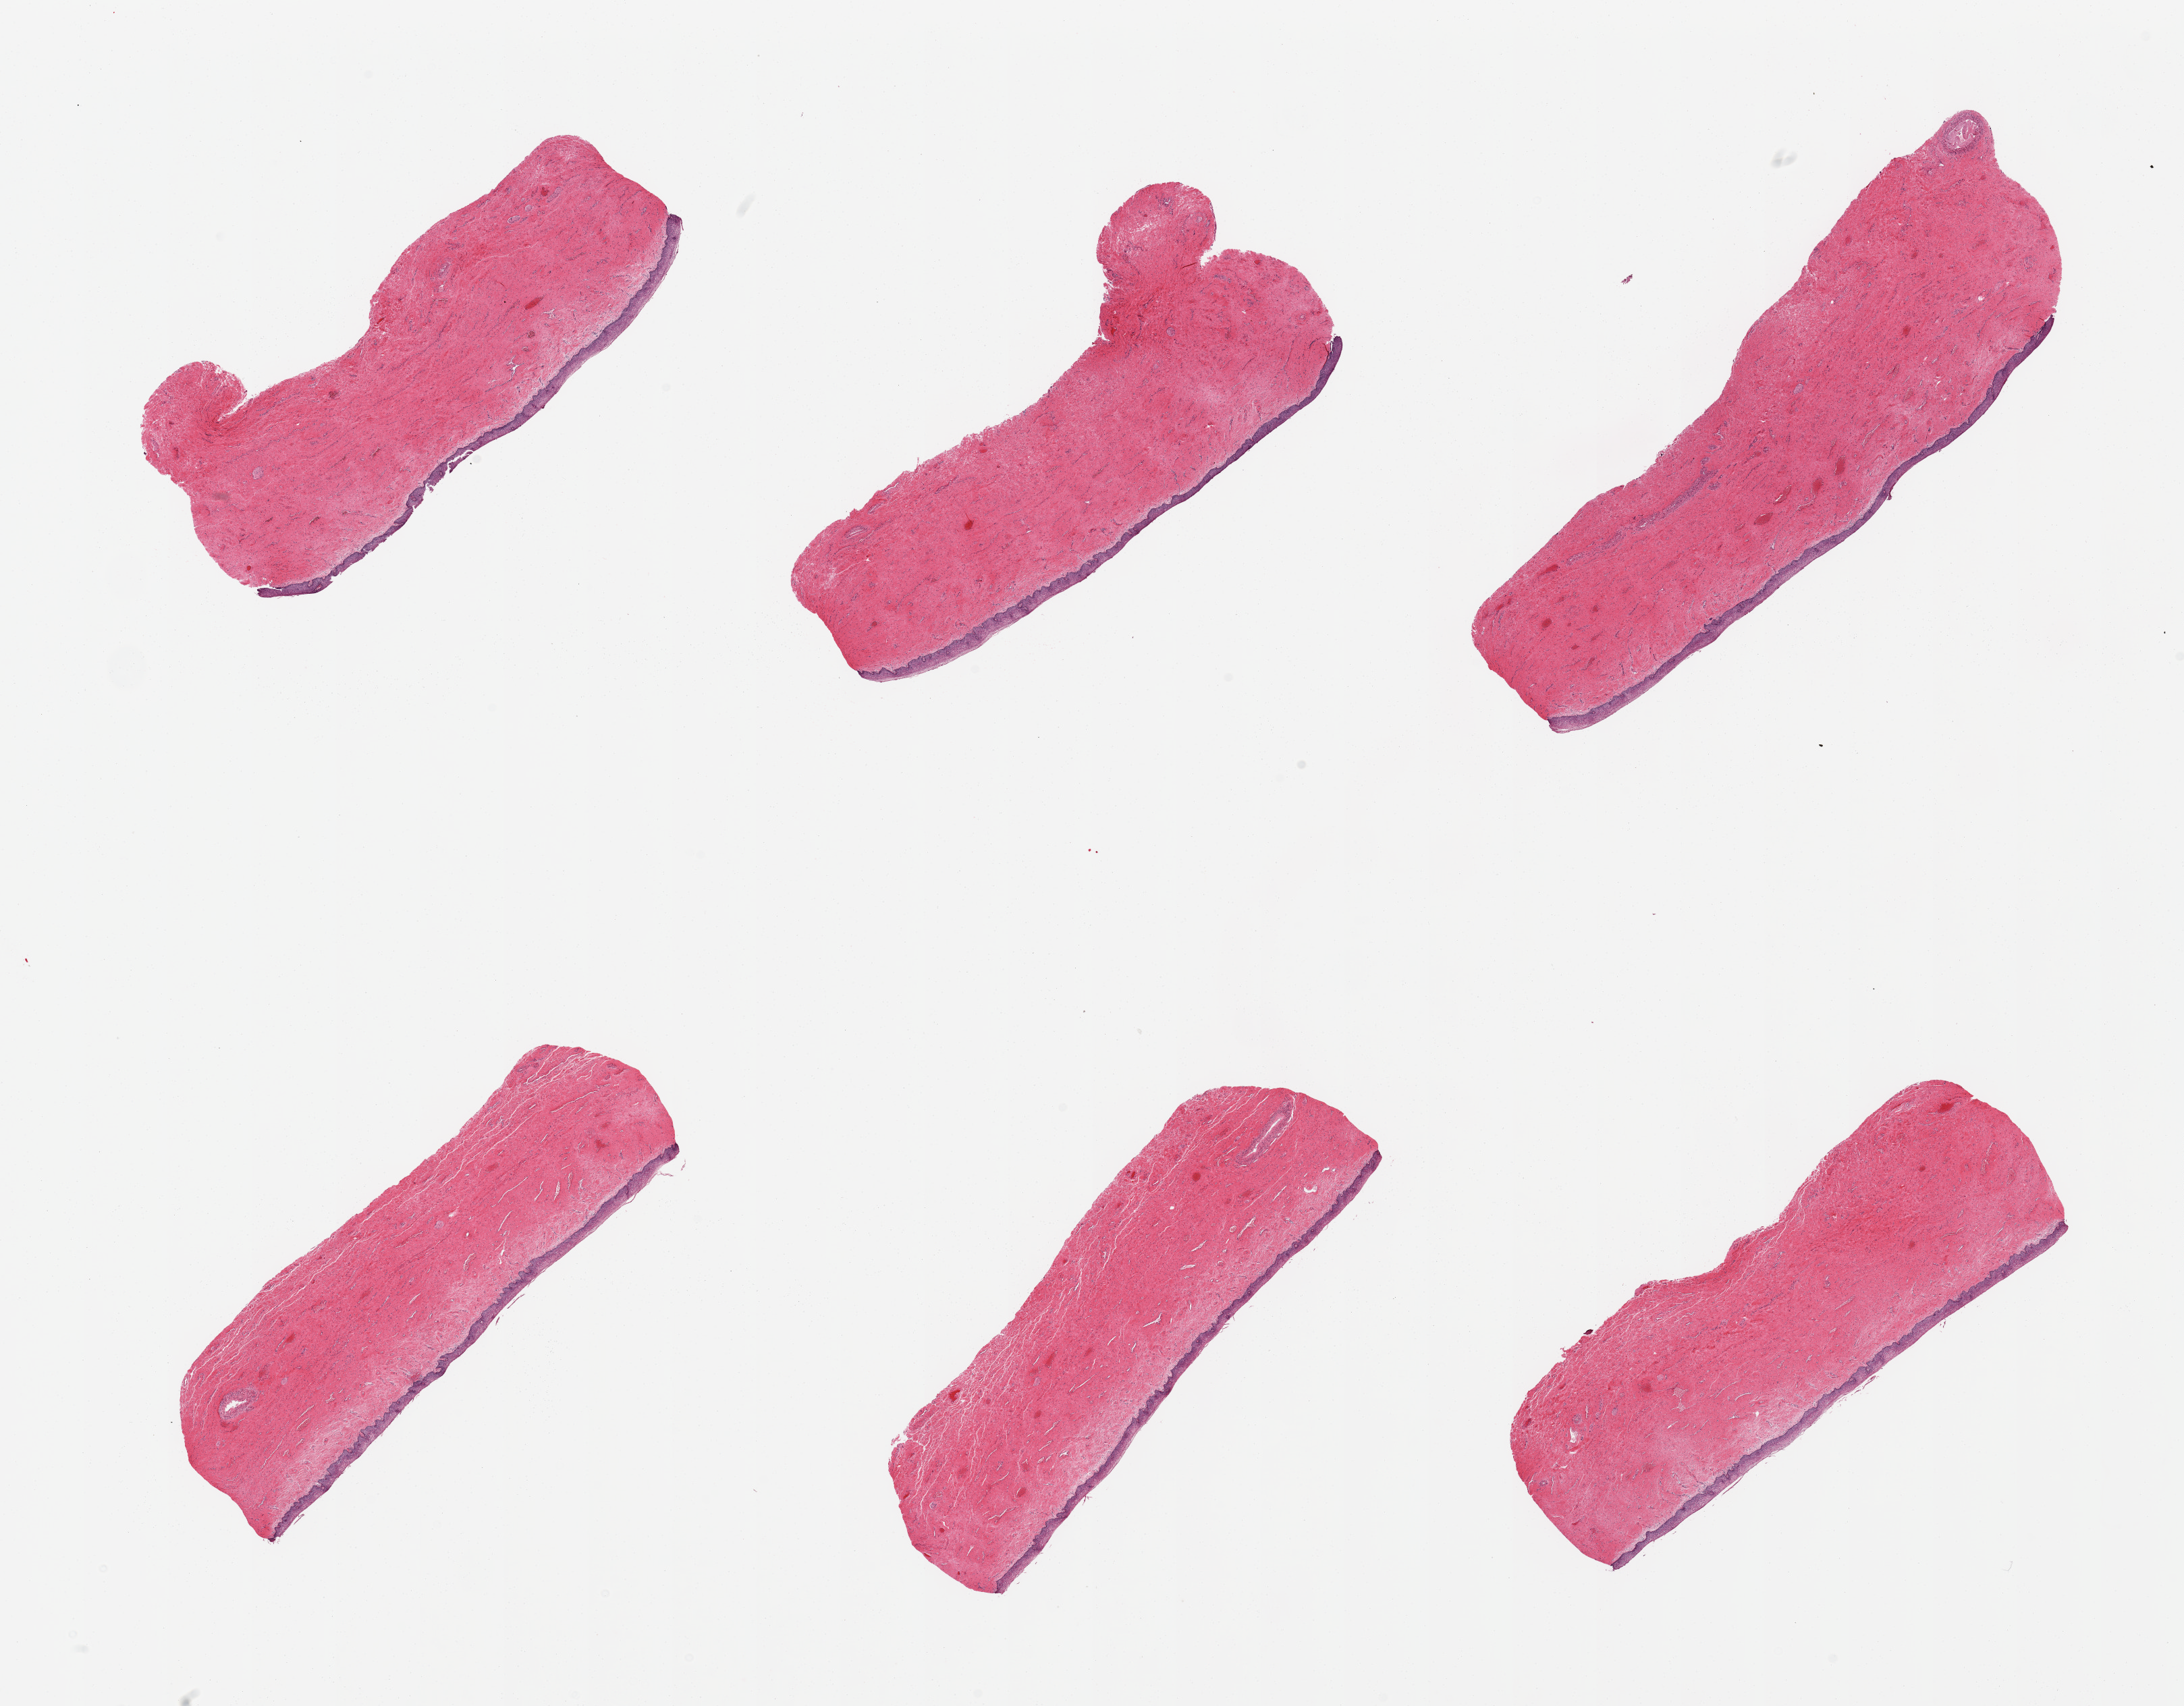
Hematoxylin and eosin (H&E) whole-slide image — shown as a low-resolution overview of the whole scanned area (about 25.6 x 20.0 mm, slide scanned at 20x). PAXgene-fixed paraffin-embedded (PFPE) section. Sampled site (target tissue): vagina. Tissue donor sample. Donor: female.
• reviewer comment on this tissue sample: 6 pieces, squamous mucosa up to ~0.2mm